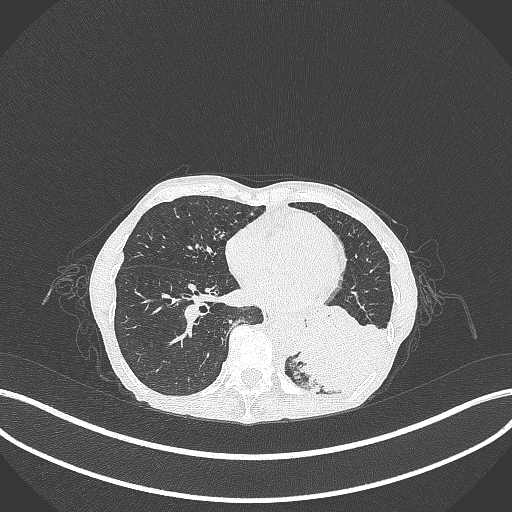
Chest CT, one axial slice; slice 96 of 347 in the series (ordered by position); reconstruction kernel B70f; lung window (W 1500 / L -600 HU); 1 mm slice thickness; 512 × 512 image matrix, field of view 400 × 400 mm. Patient: female, 70 years. Case-level facts recorded for this patient, not image findings: clinical TNM (as recorded): T3 N0 M0; histopathological grade: G3.
Annotated regions visible in this slice (rectangle marked by the reading radiologist):
- lung tumour (recorded histology: small cell carcinoma): bounding box (x1, y1, x2, y2) in pixels: (293, 316, 392, 402)